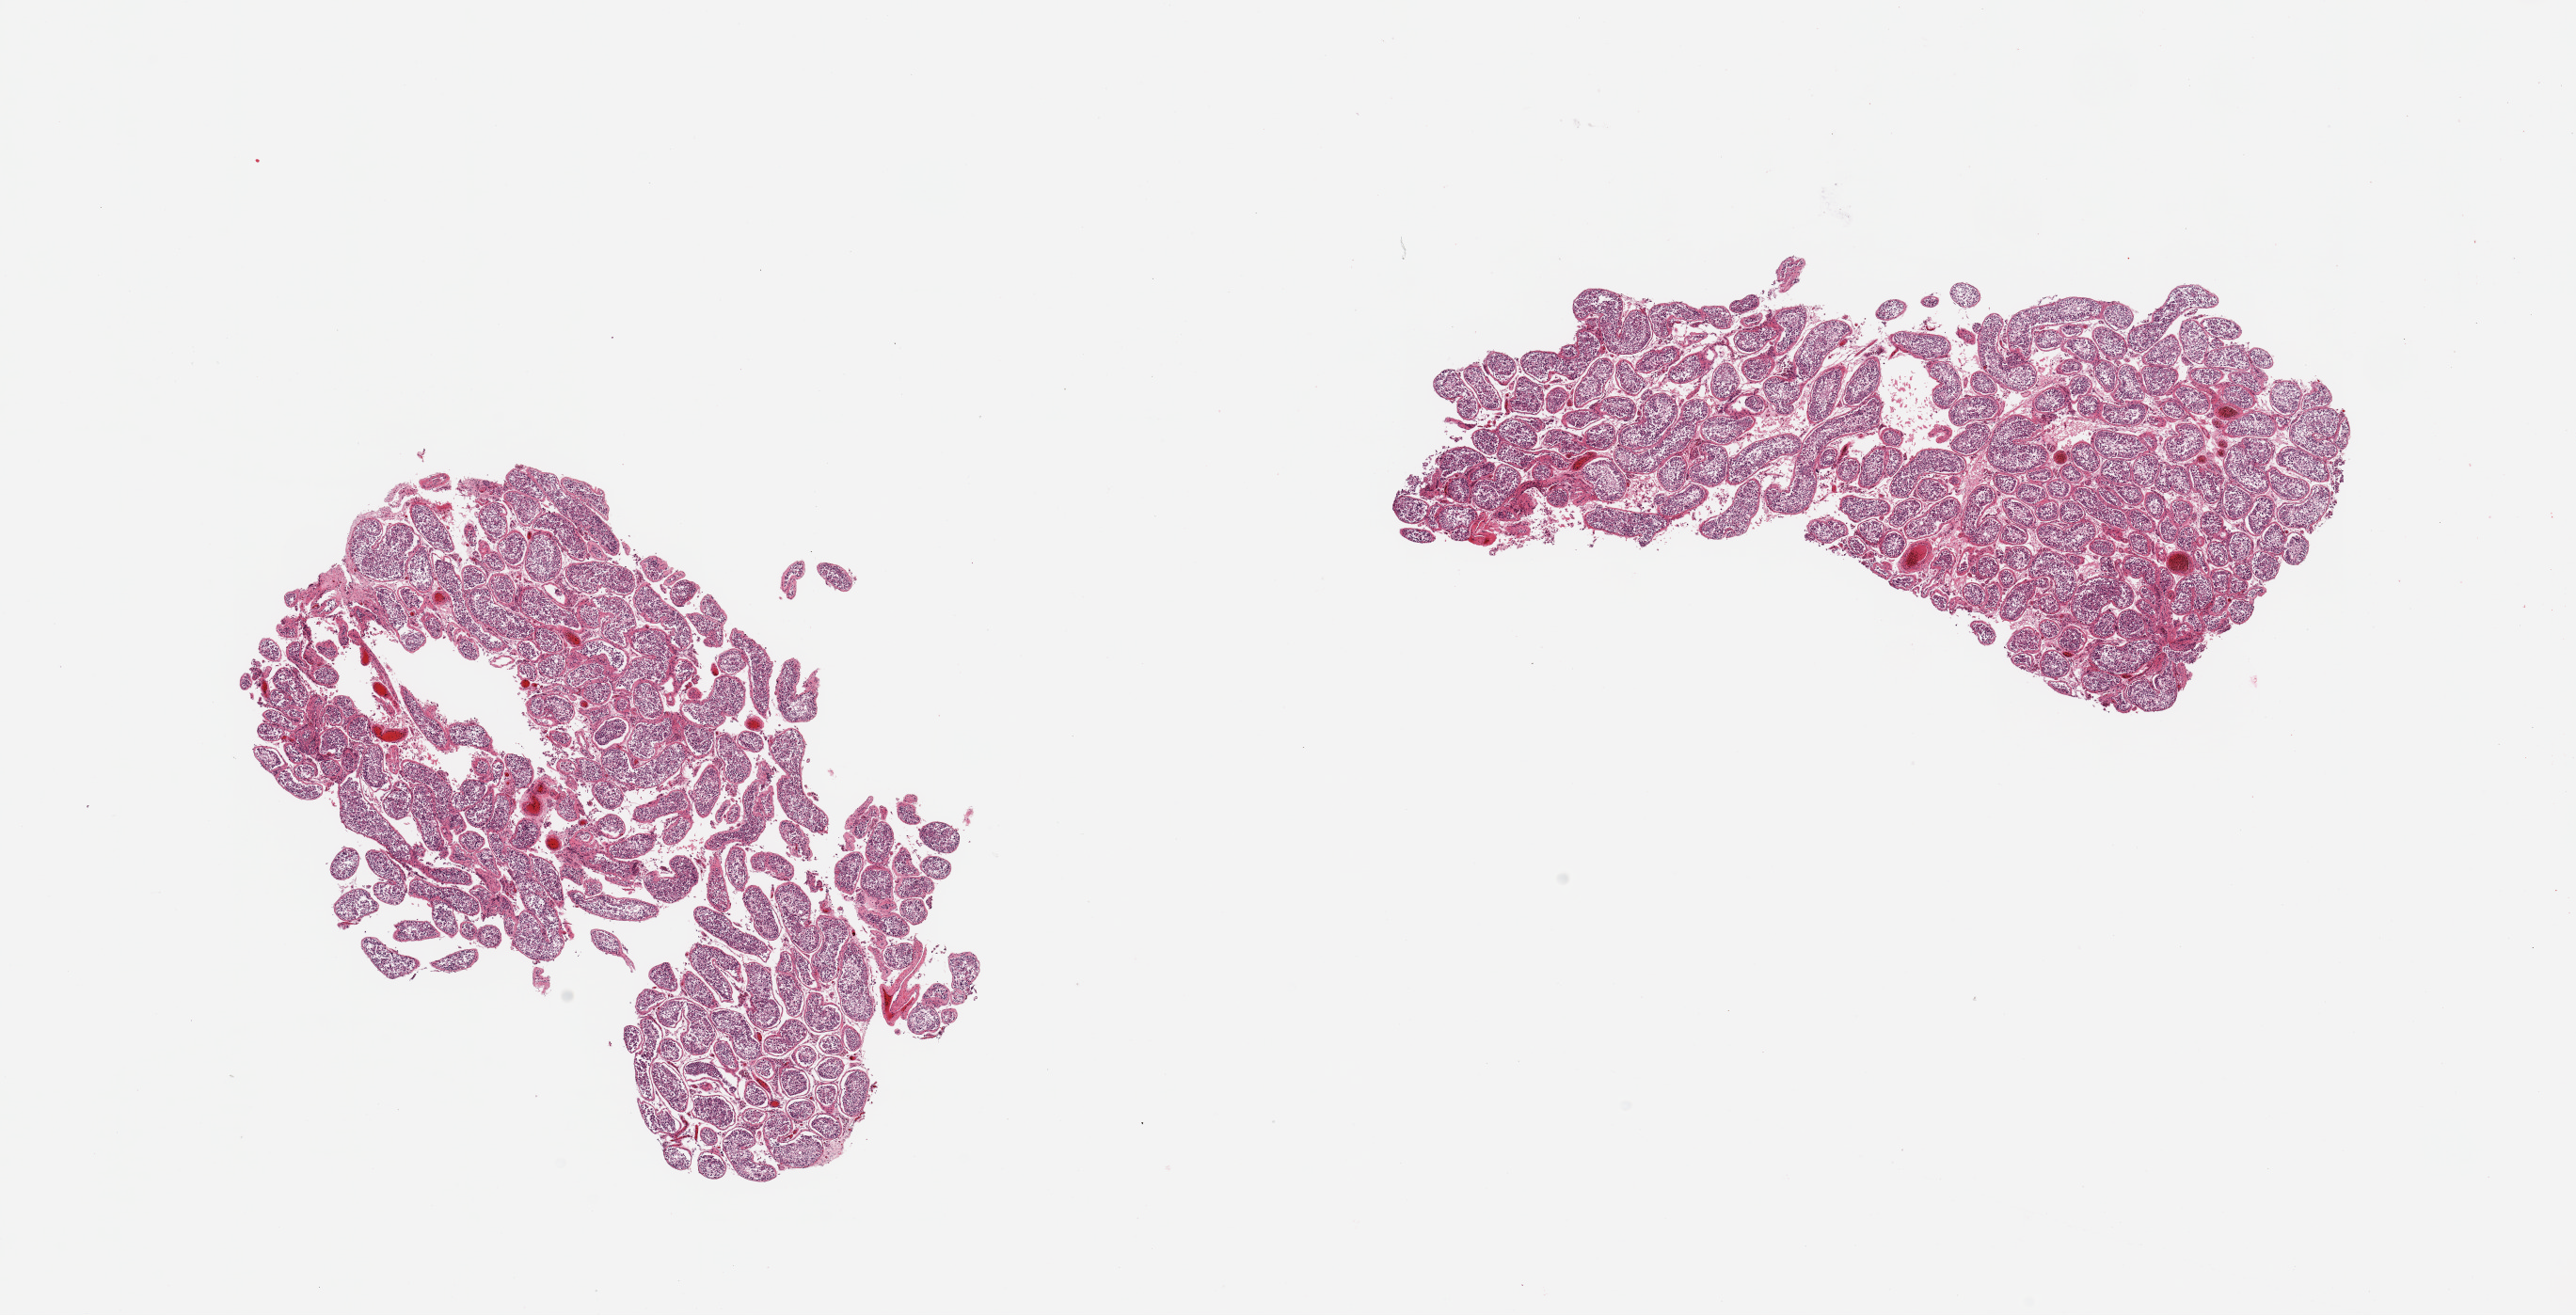
Digitized haematoxylin and eosin-stained section, shown as a low-resolution overview of the whole scanned area (about 21.7 x 11.1 mm), PAXgene-fixed paraffin-embedded (PFPE) section, section of testis (target tissue), tissue donor sample. Male donor.
Pathologist's review note for this sample: 2 pieces, no abnormalities.